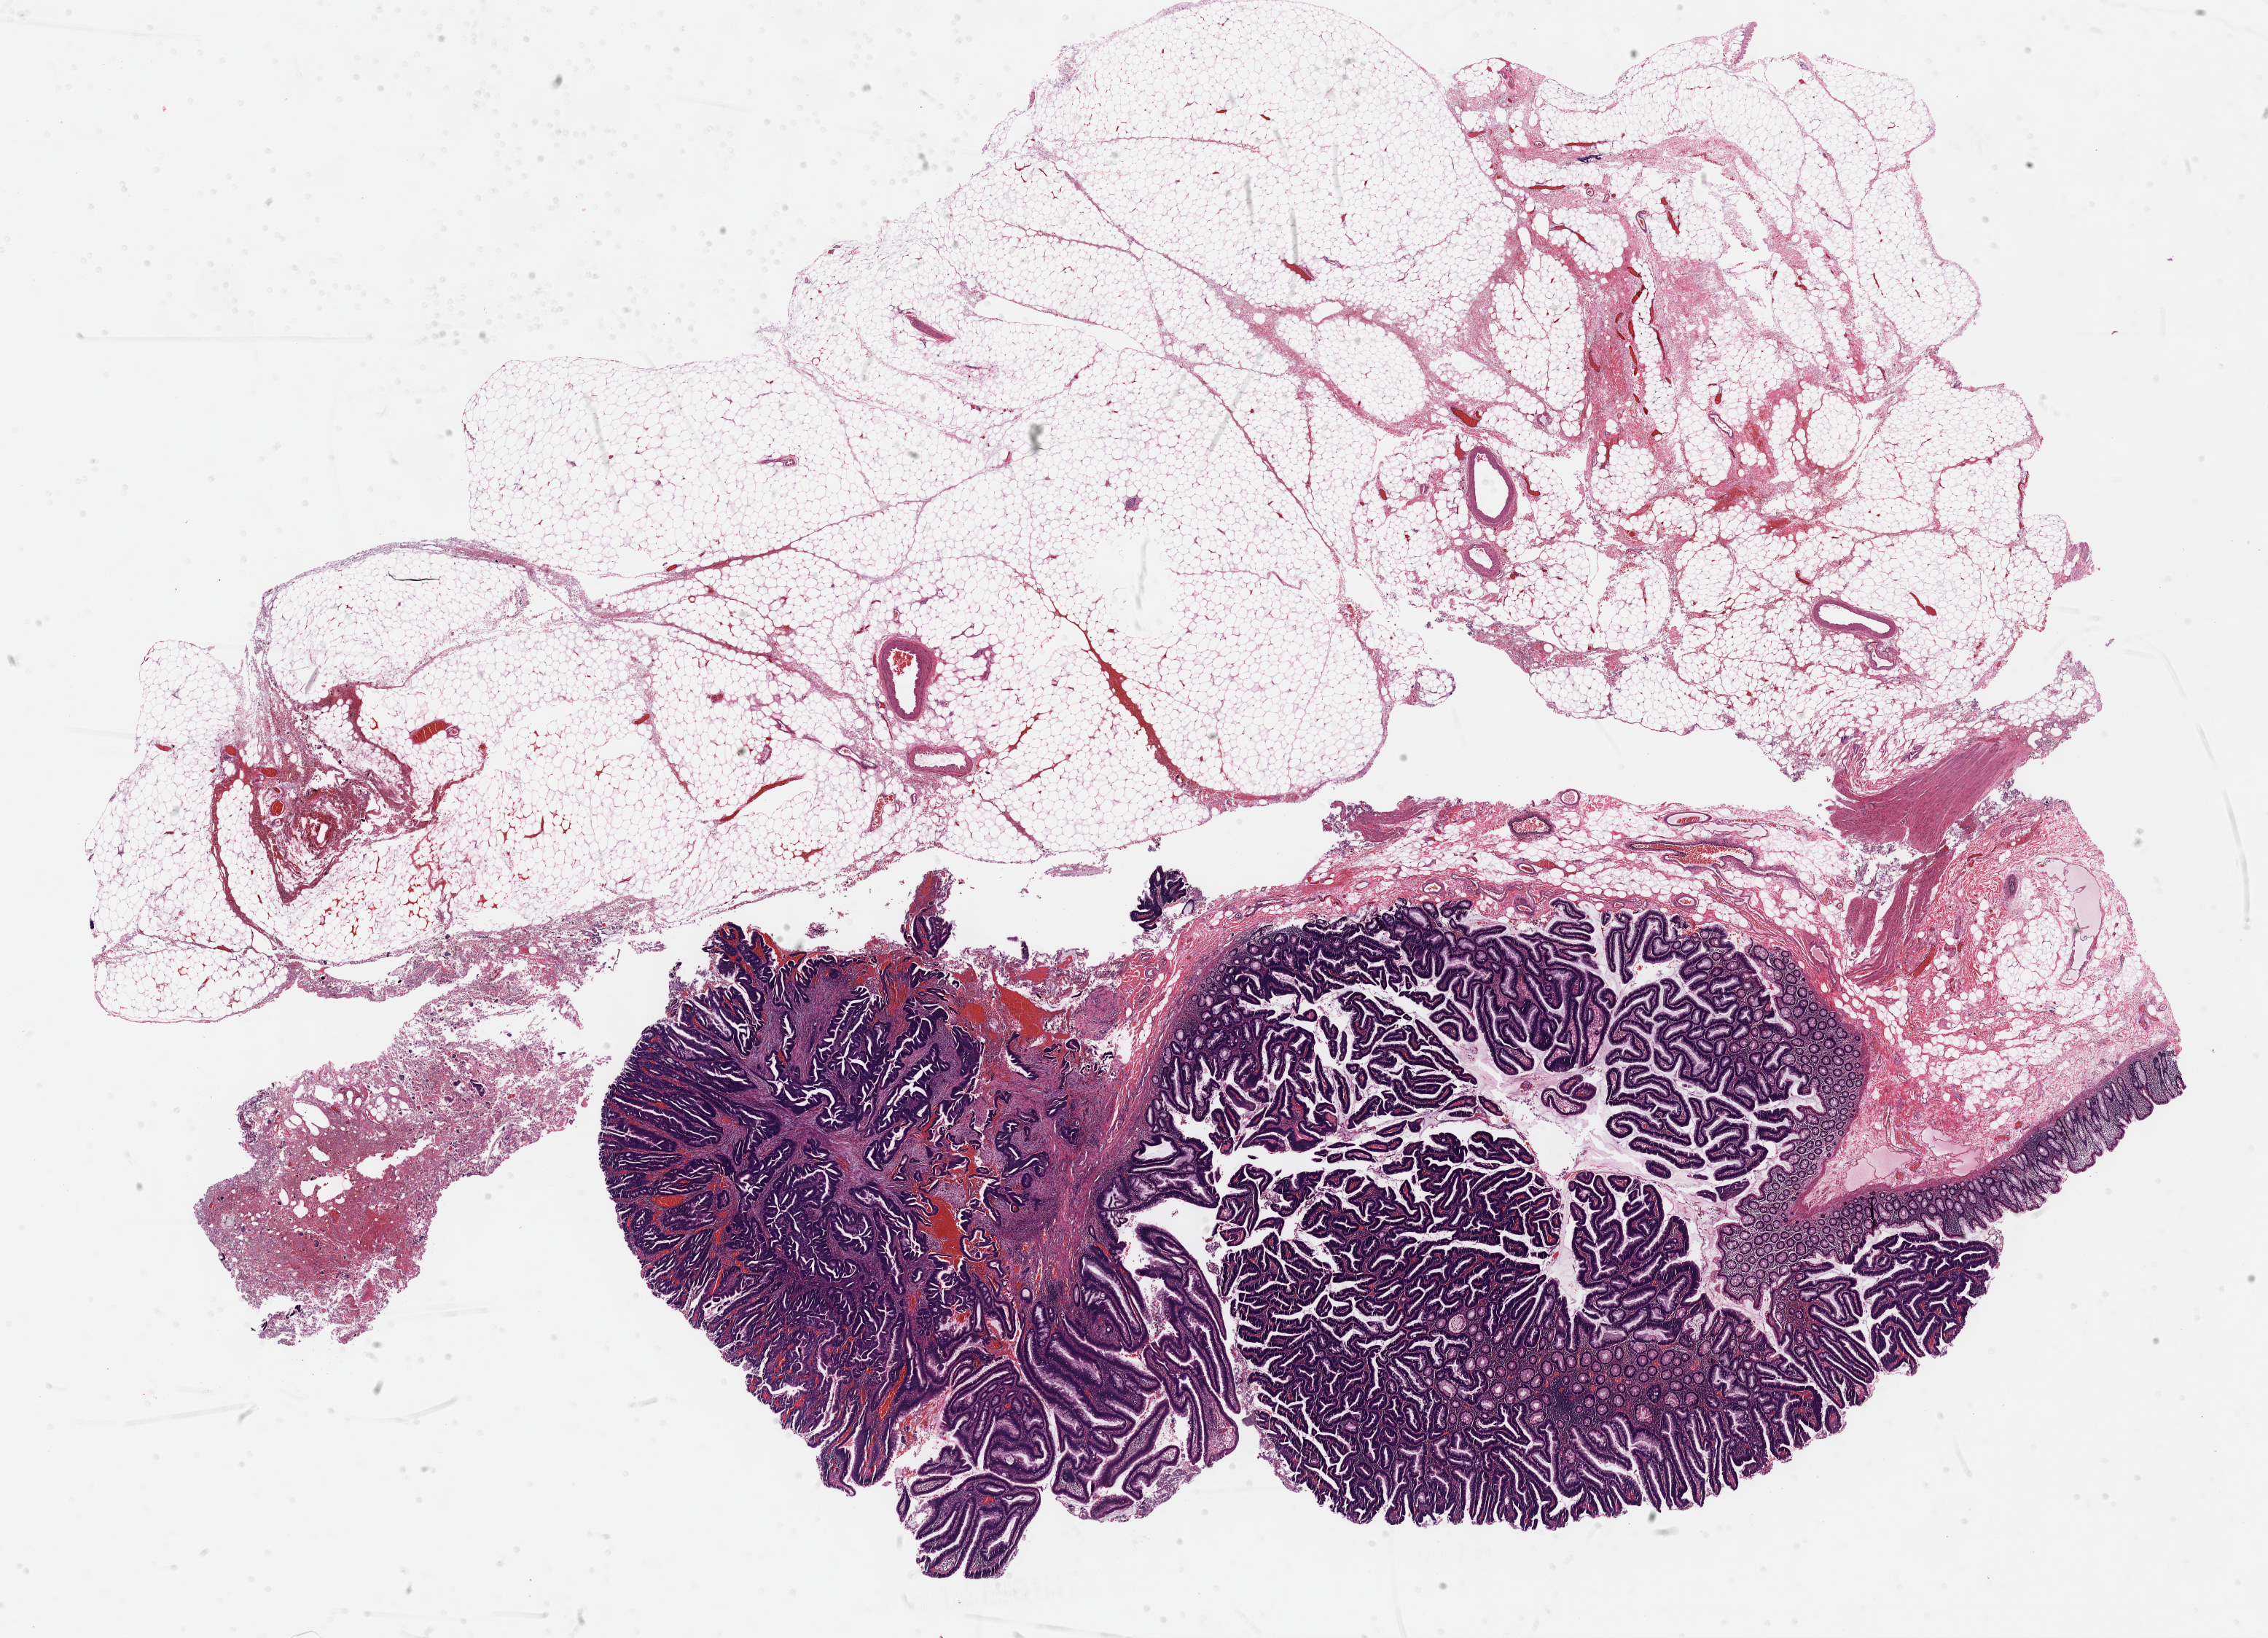
Hematoxylin and eosin (H&E) stained whole-slide image, shown as a low-resolution overview of the whole scanned area (about 25.2 x 18.2 mm); formalin-fixed paraffin-embedded (FFPE) diagnostic section; primary tumour sample from the colon. Male, age 67 years at initial diagnosis.
• pathologic diagnosis: Adenocarcinoma, NOS (ascending colon)
• AJCC pathologic stage: IIIB (7th edition)